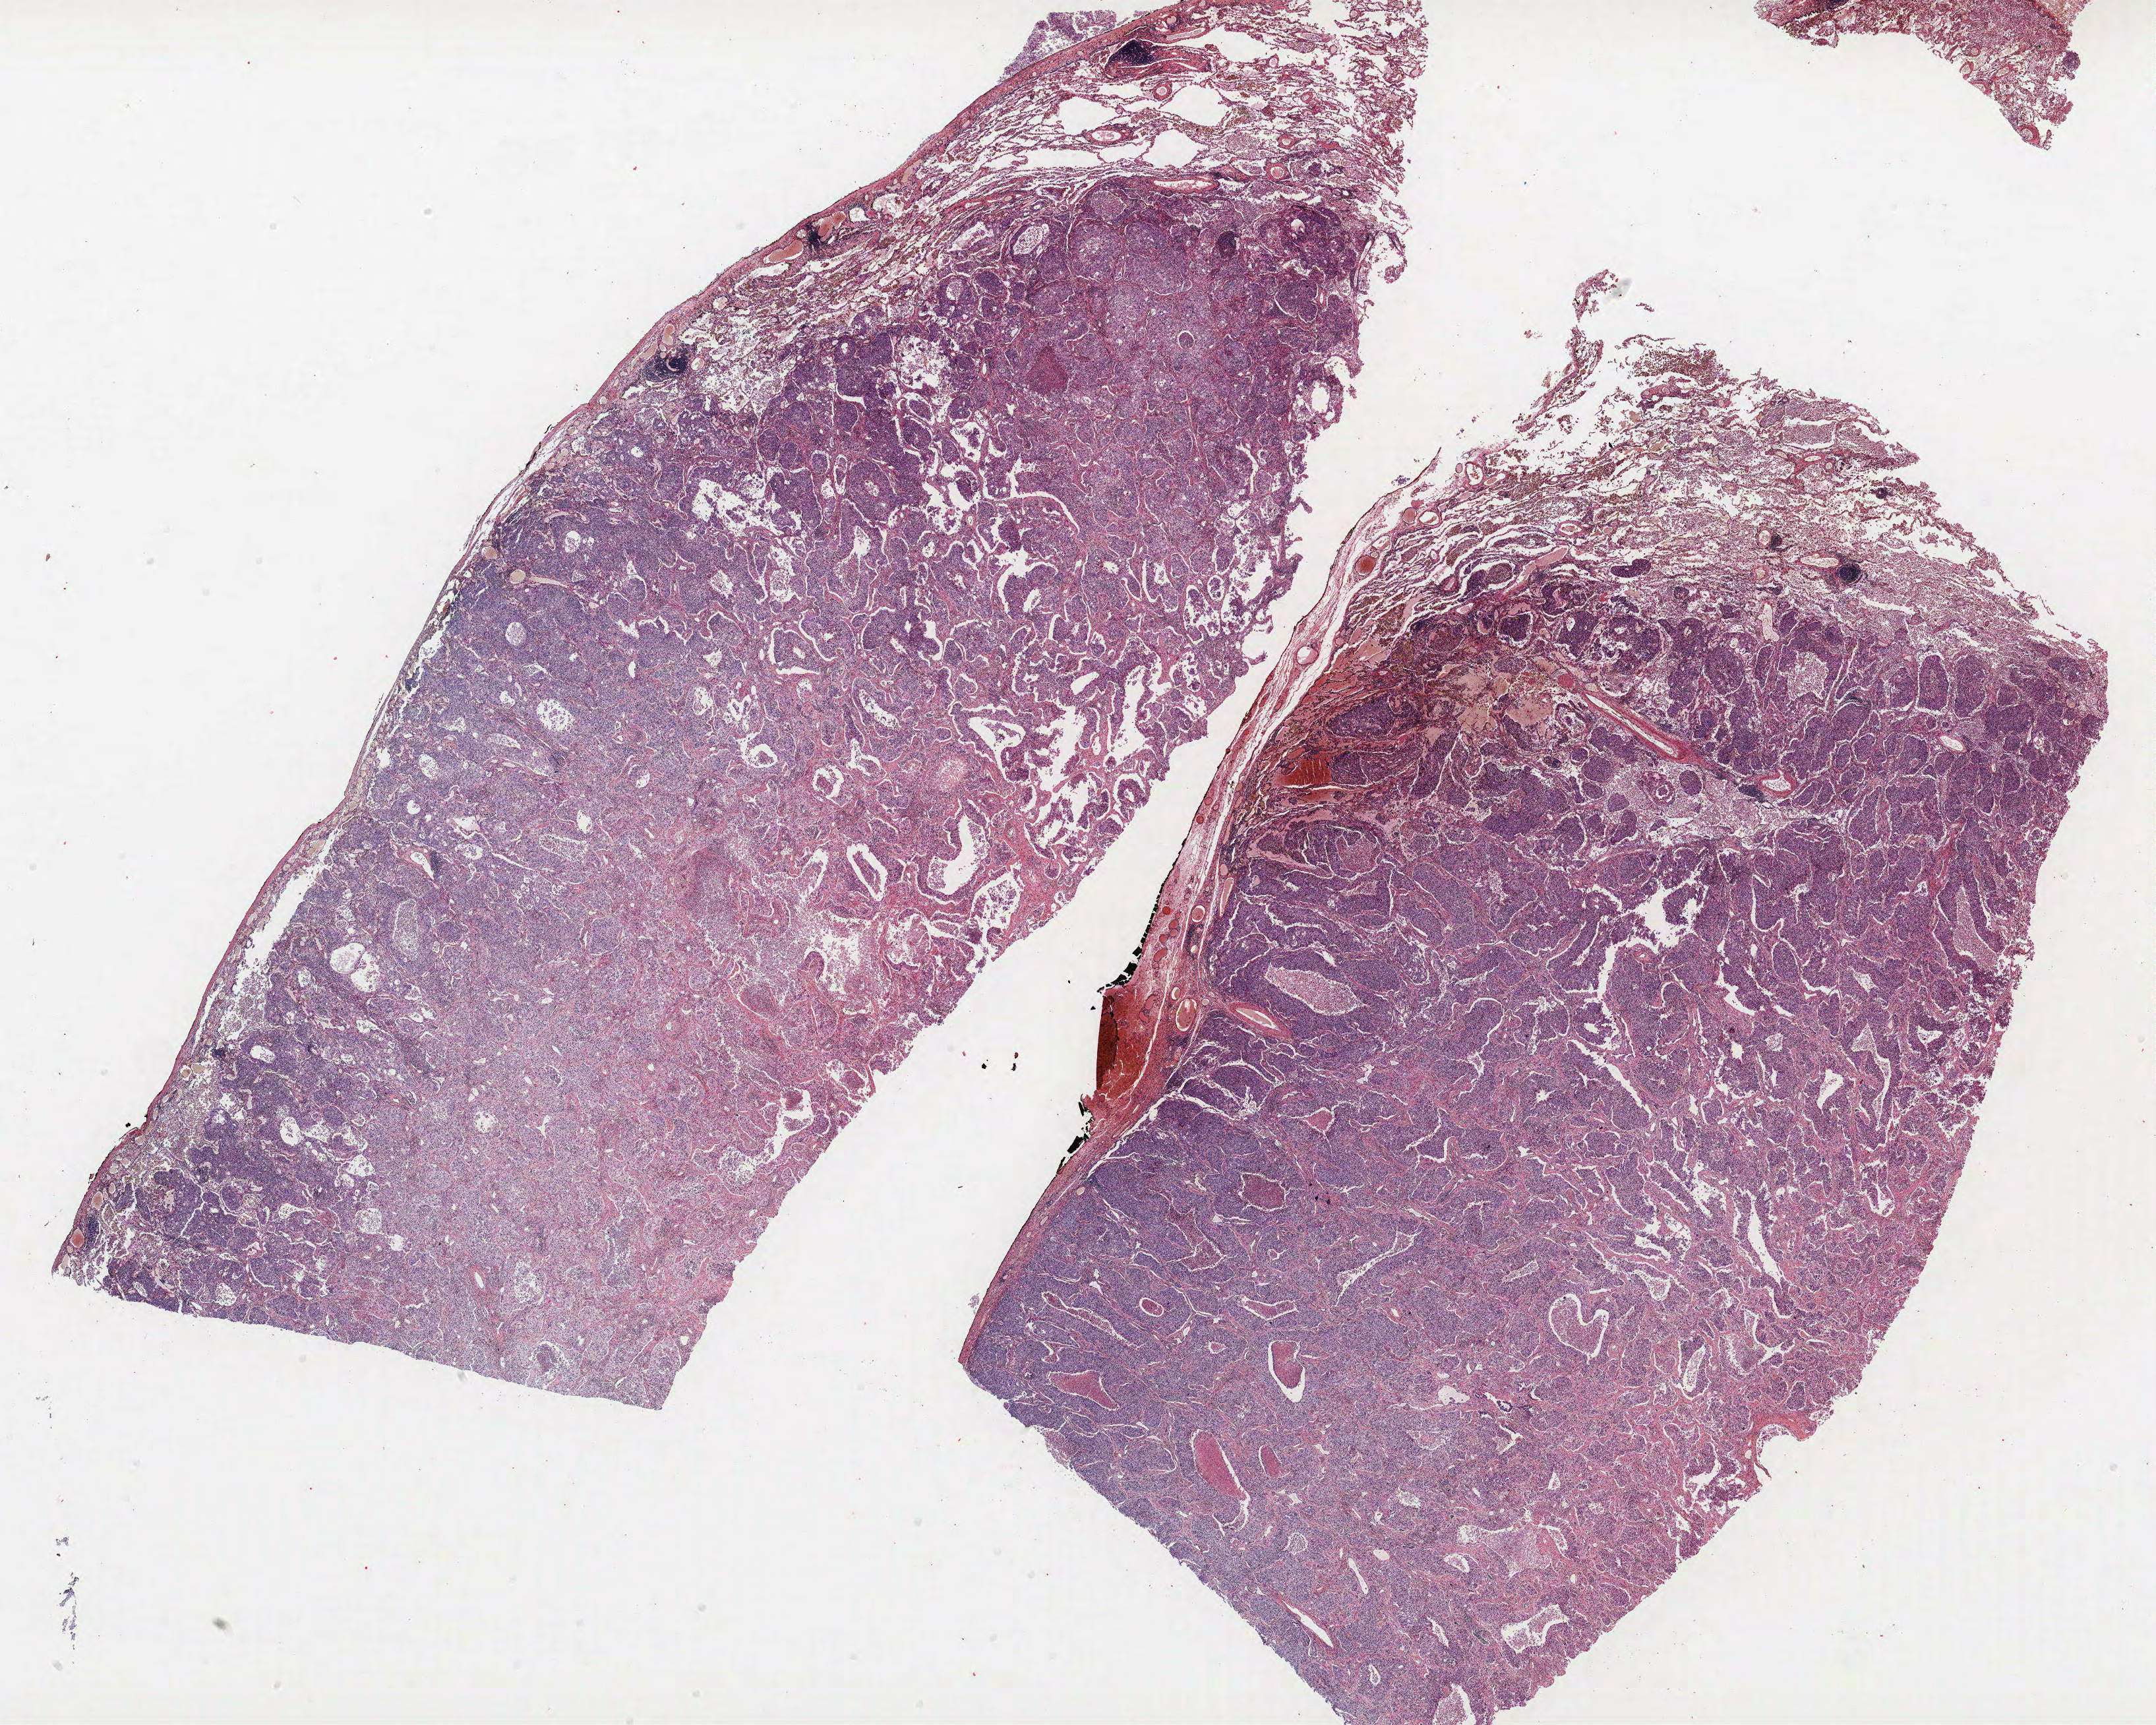
H&E whole-slide image, a low-resolution overview of the entire scanned area, about 26.2 x 20.9 mm (acquisition: 40x scan); formalin-fixed paraffin-embedded (FFPE) section; lung tissue. Male patient, aged 56 at enrolment. Current smoker at enrolment. Grade: poorly differentiated (G3).
- stage (AJCC 6th edition): IIB
- participant's lung-cancer diagnosis: Adenocarcinoma, NOS
- primary tumour location (clinical record): right upper lobe
- tumour size (pathology): 60 mm